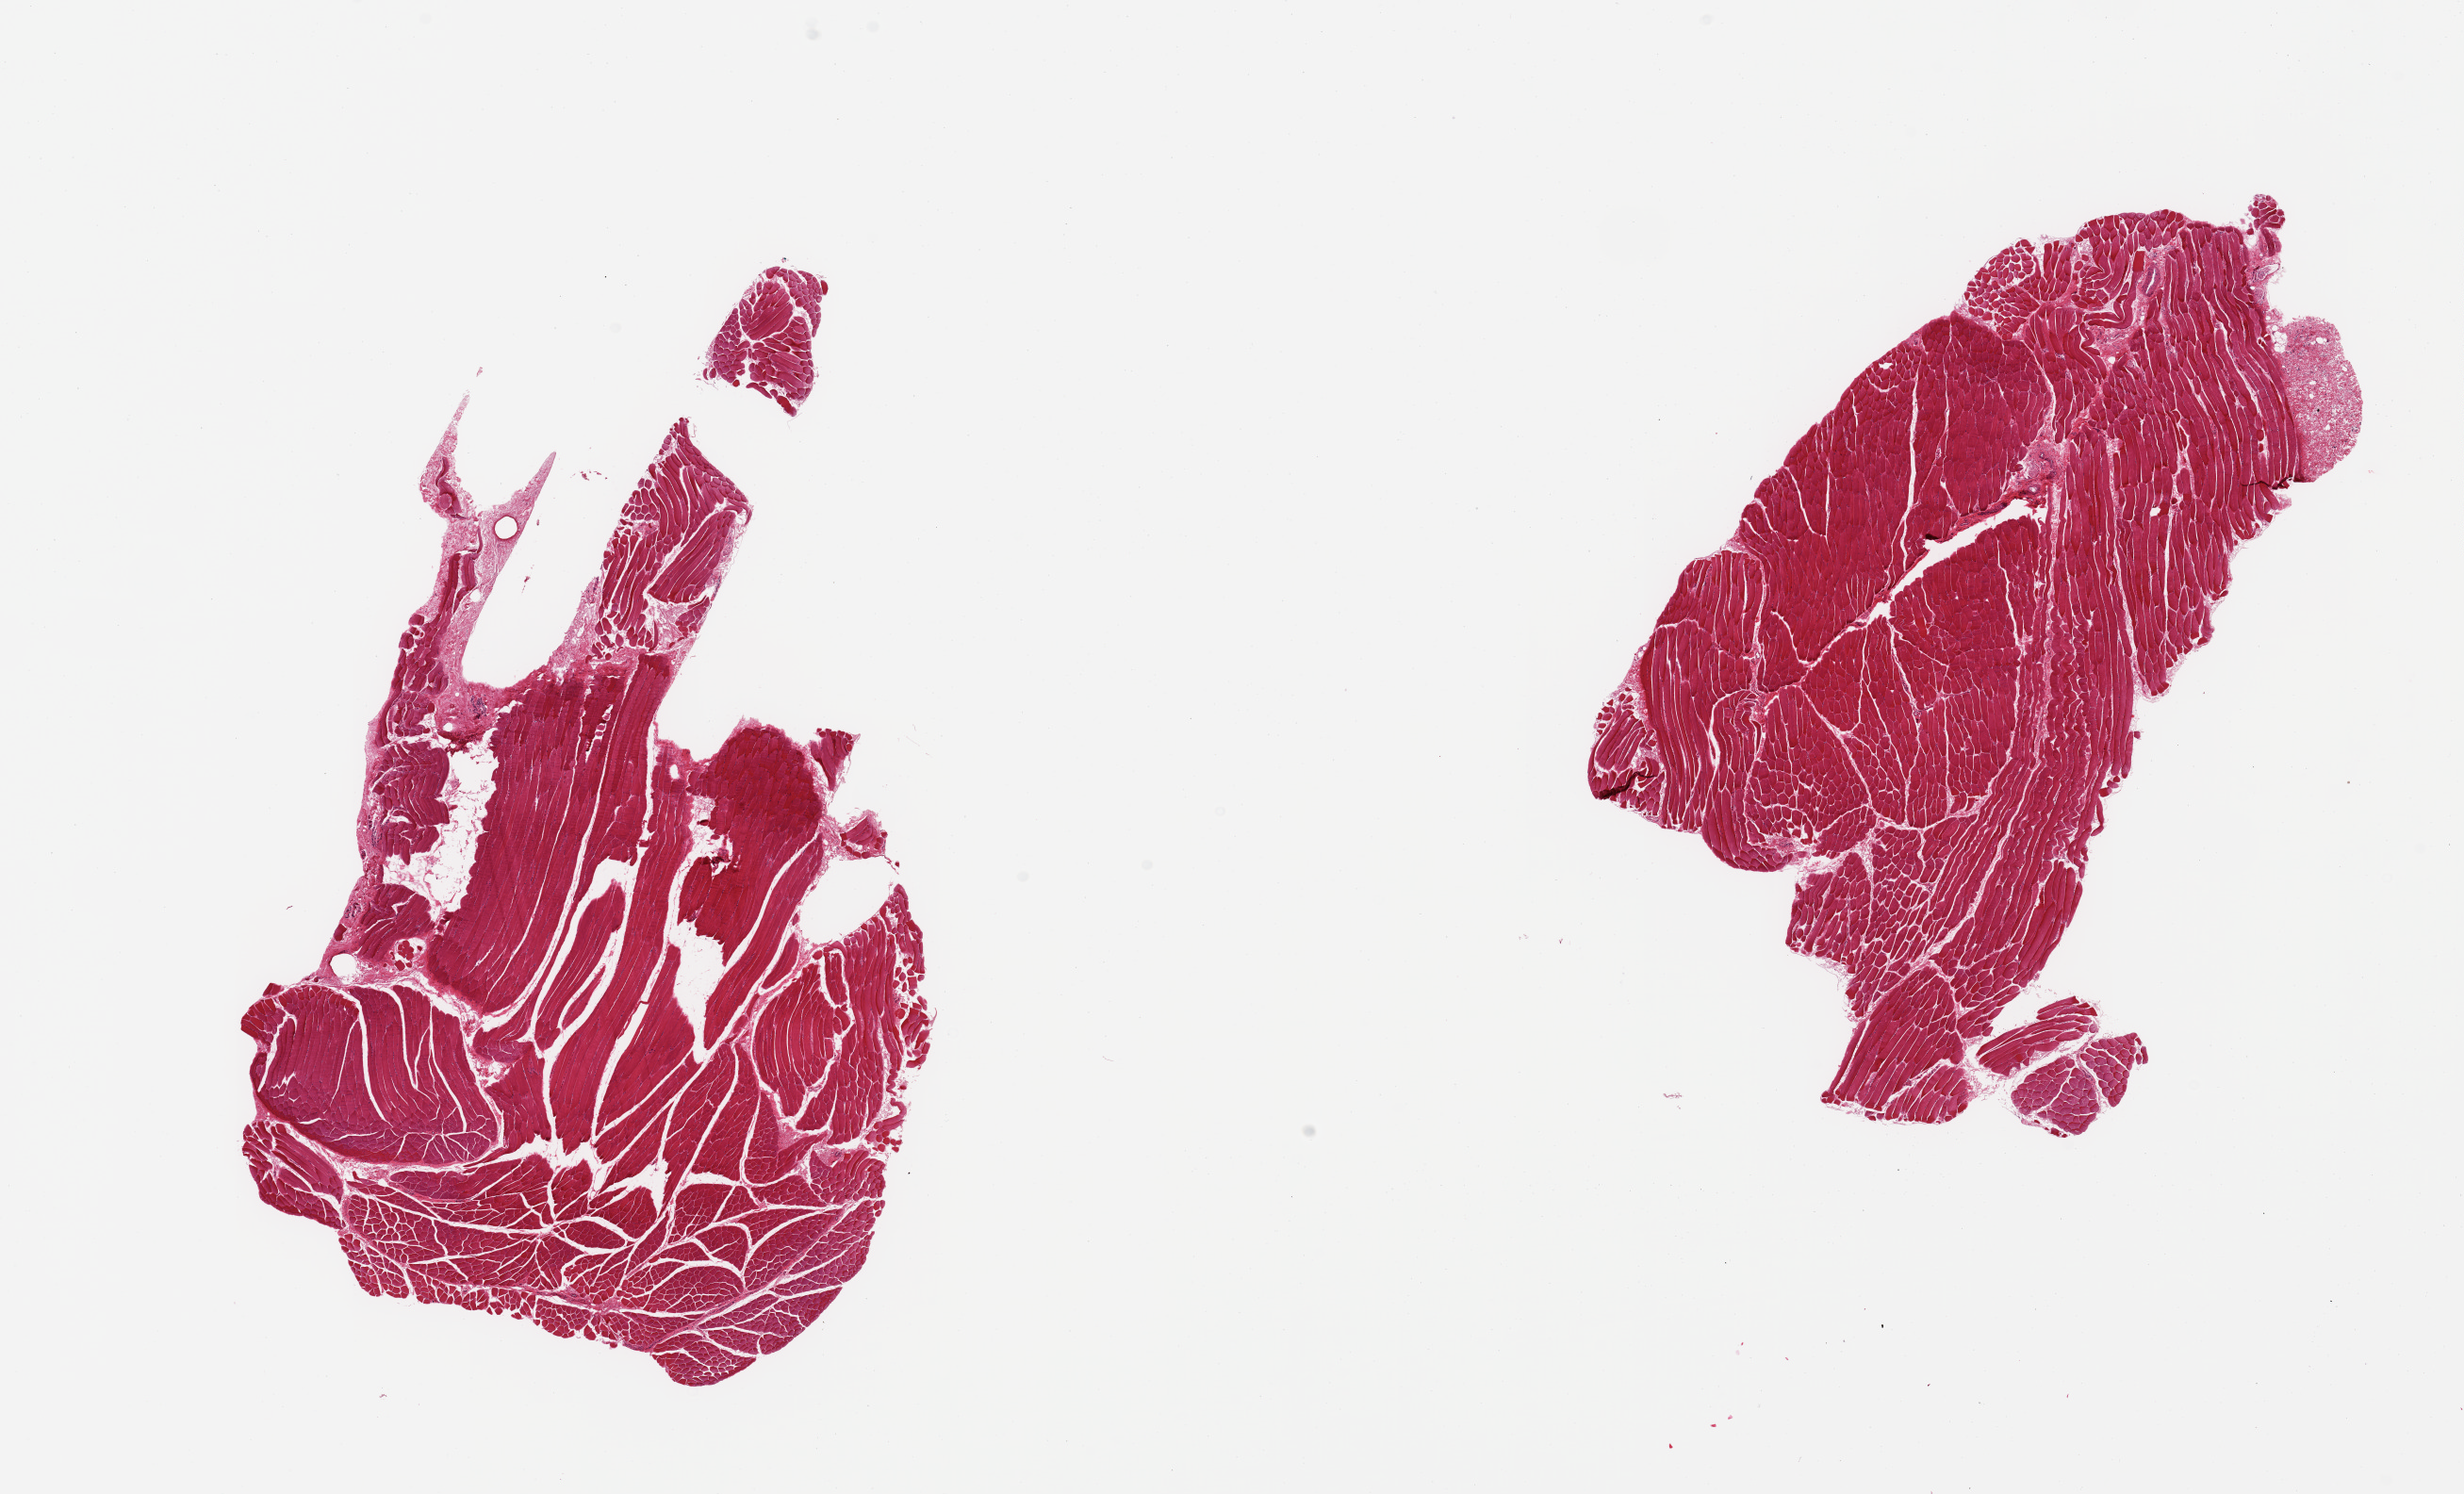
Digitized hematoxylin and eosin (H&E)-stained section — whole scanned area (about 20.7 x 12.5 mm, slide scanned at 20x) shown as a low-resolution overview. Donor: male.
Specimen: PAXgene-fixed paraffin-embedded (PFPE) section; sampled site (target tissue): thyroid; tissue donor sample.